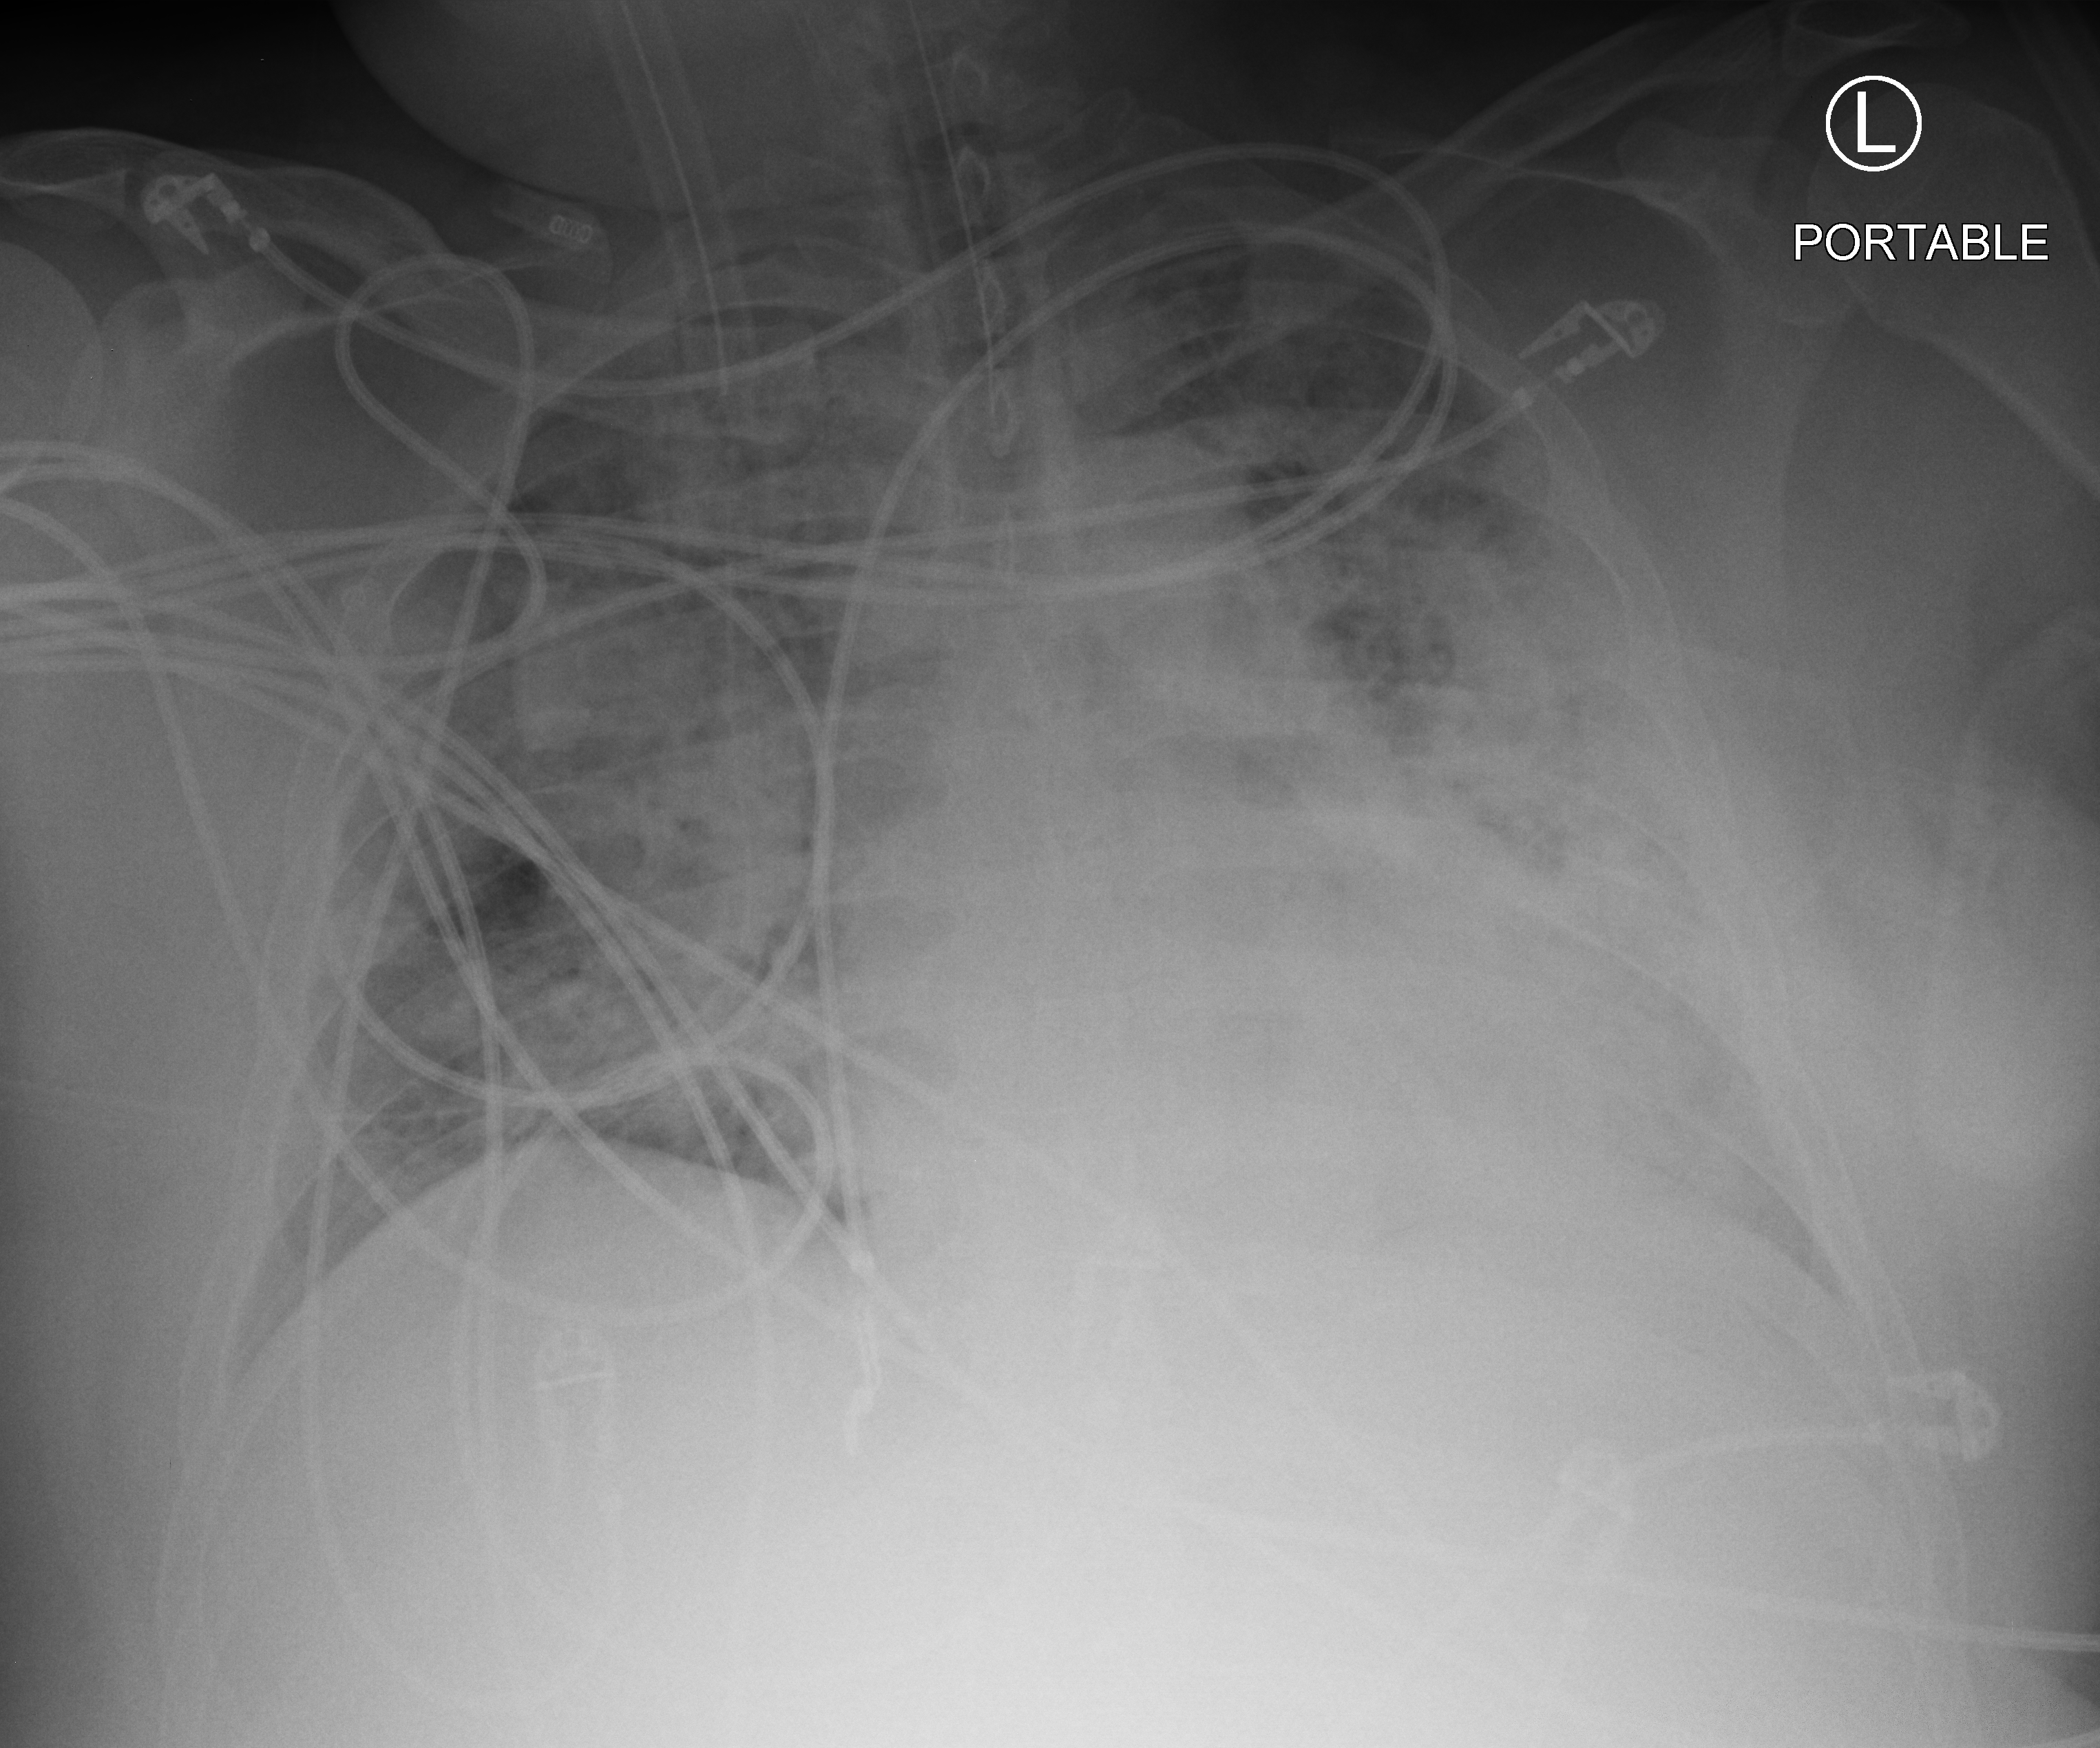
Portable chest radiograph; anteroposterior (AP) projection. Adult patient hospitalised with COVID-19, age 18–59 years.
From the hospital-stay record, not from the radiograph (when in the stay this image was taken is not recorded): length of hospital stay: 22 days; mechanically ventilated during this hospital stay: yes; chronic kidney disease (admission record): no.